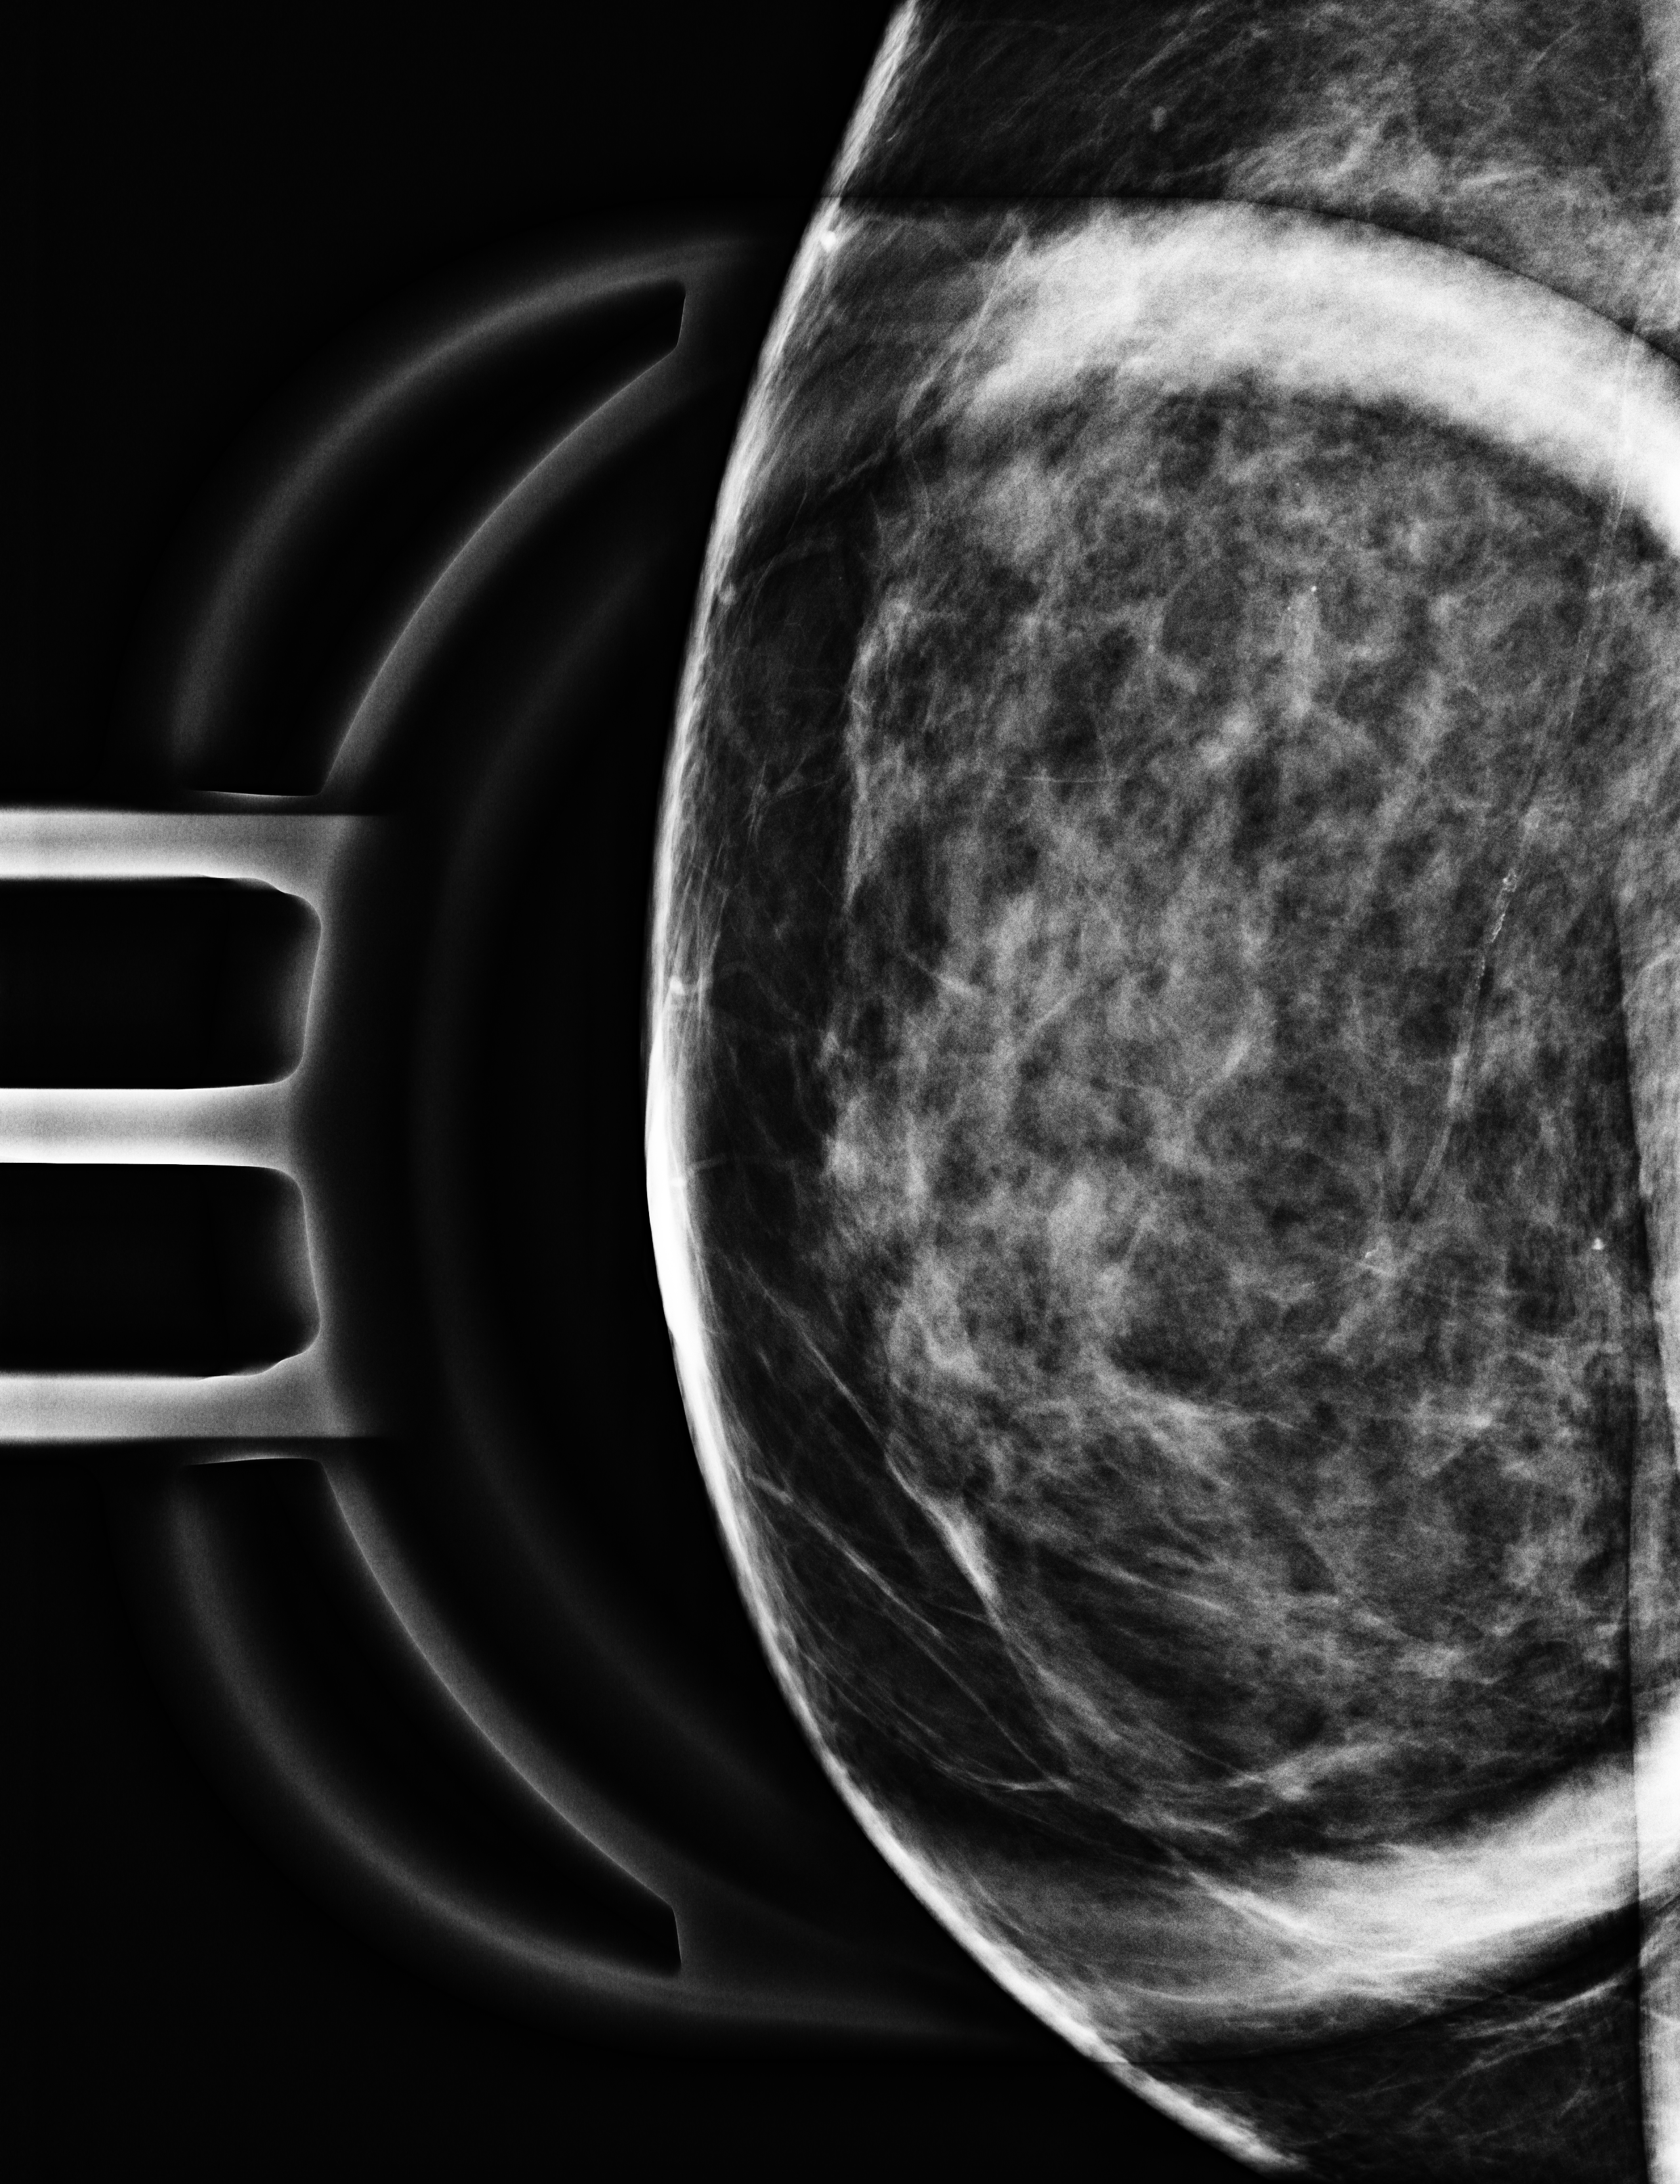
Additional work-up view, system: Selenia Dimensions. Patient aged 56 years (female).
Image type: full-field digital mammogram. Breast: right. Projection: mediolateral (ML) view, magnification.